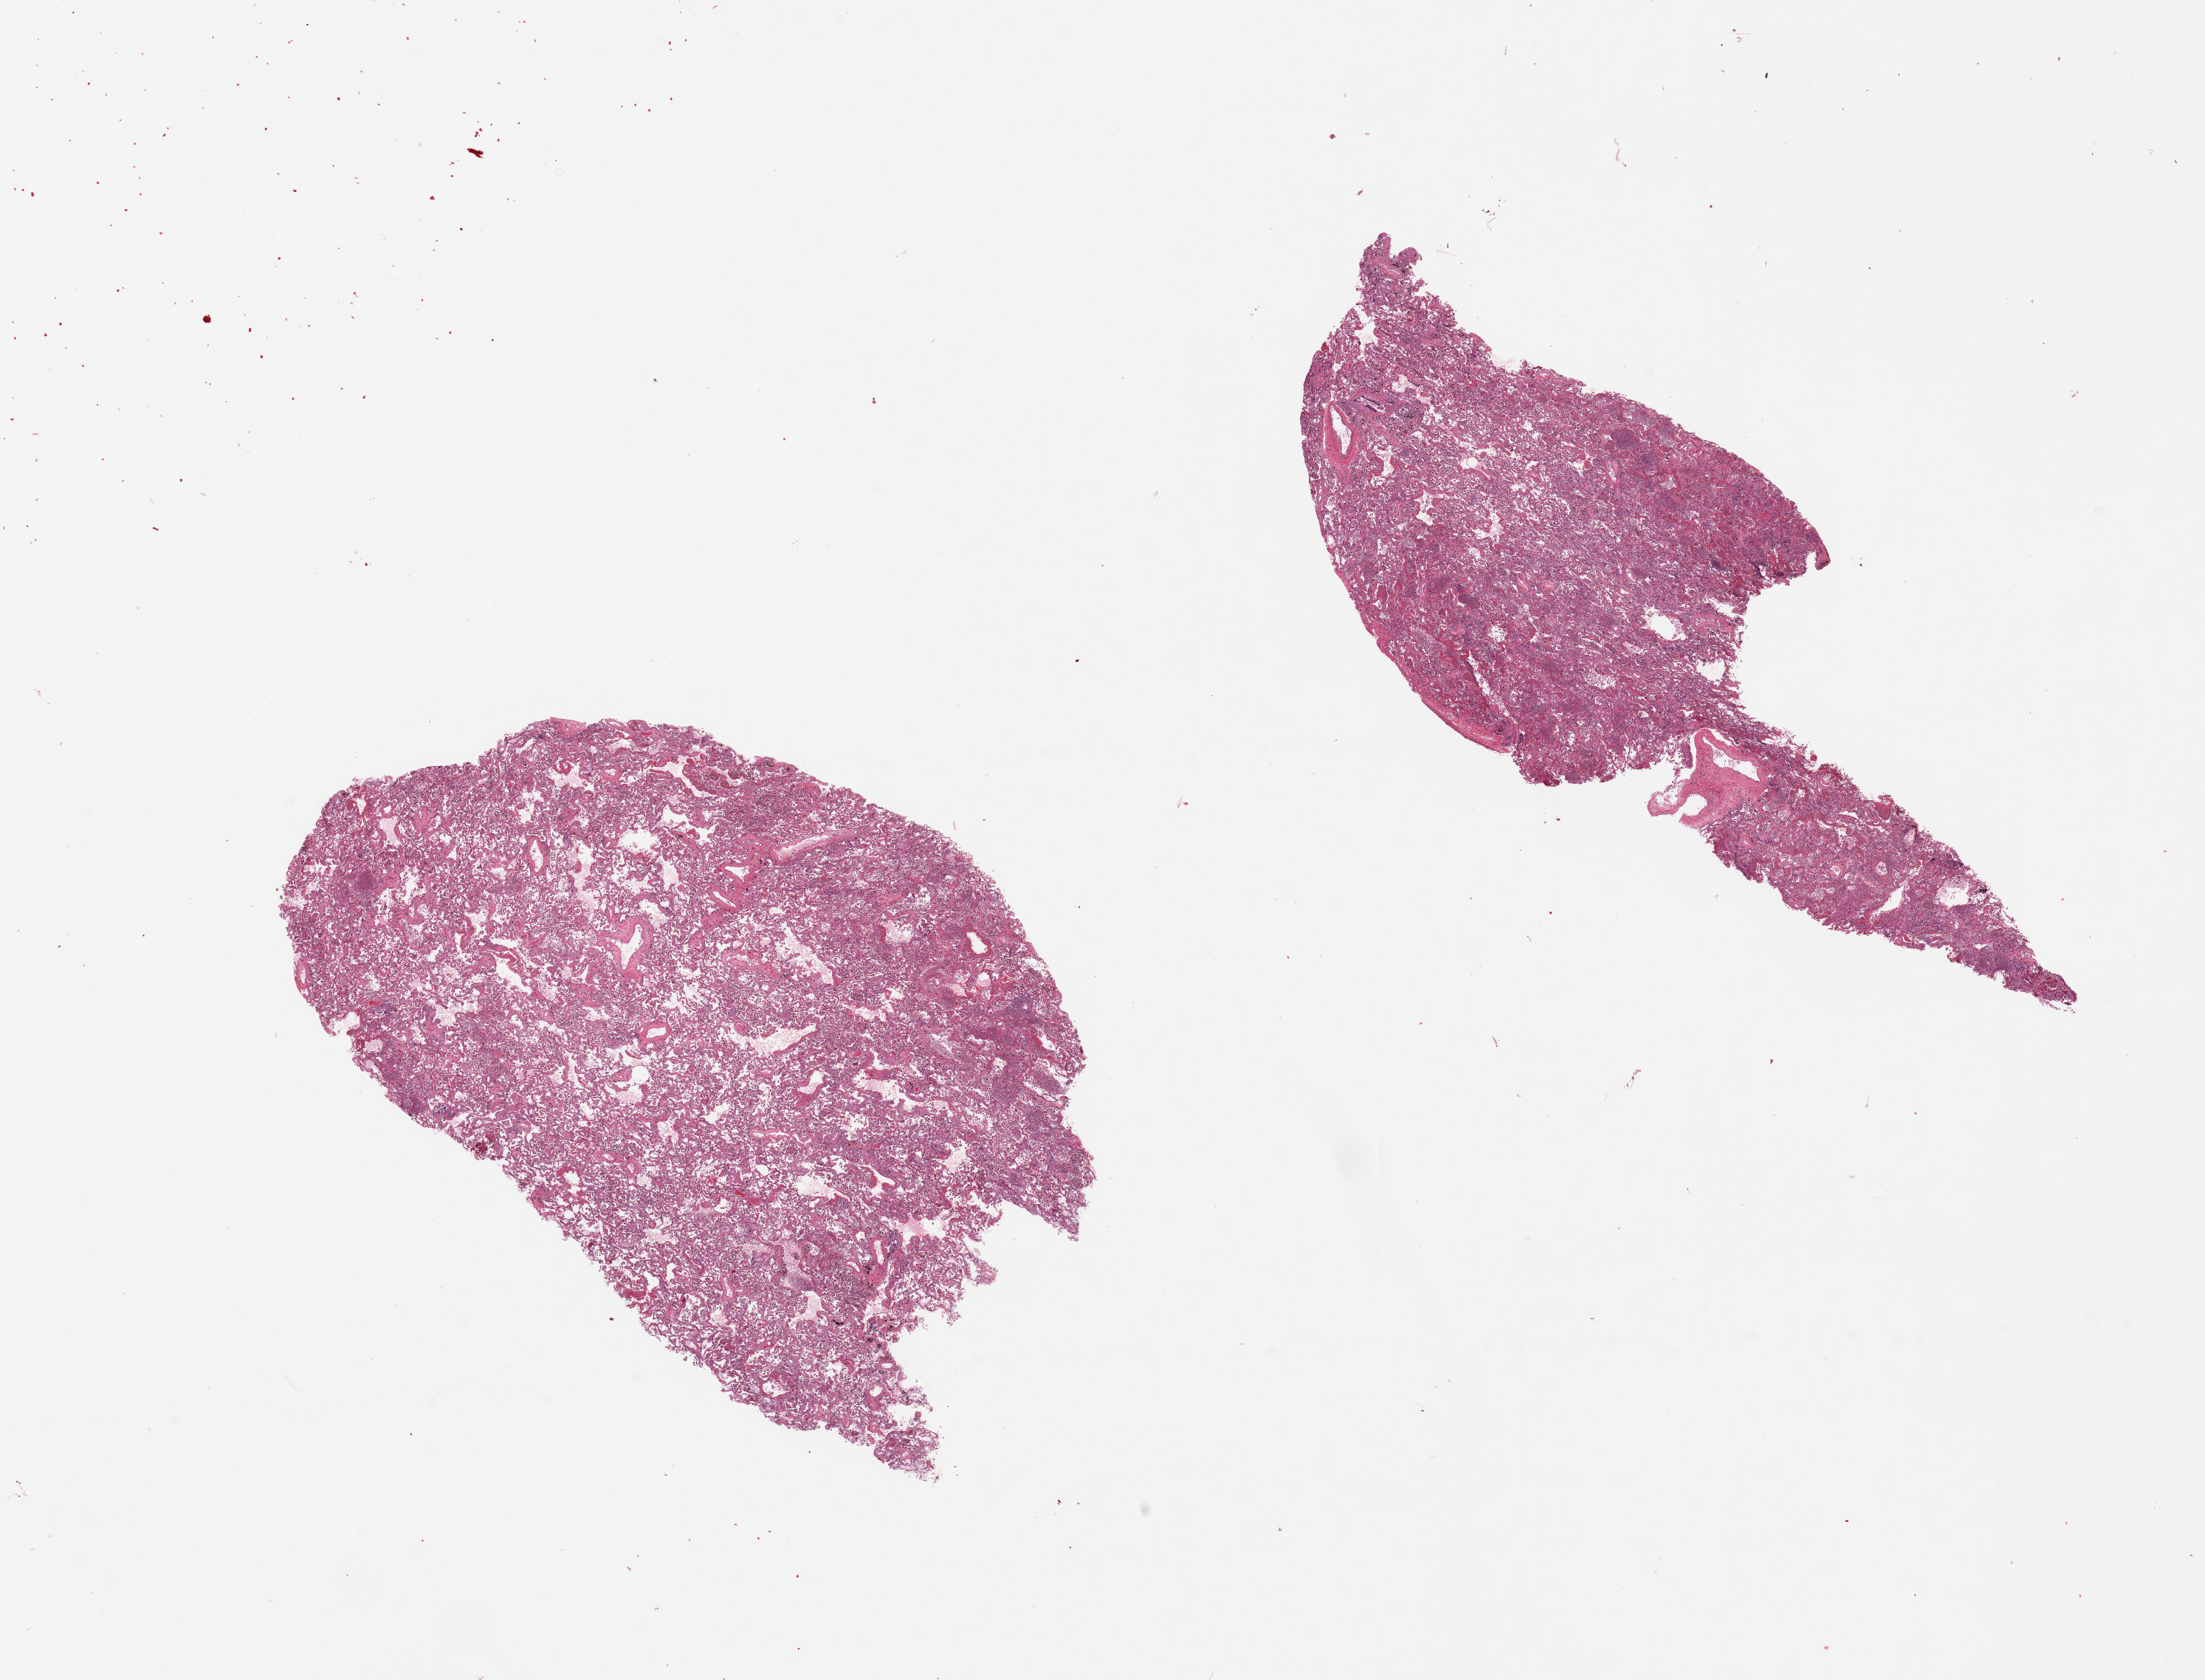
H&E whole-slide image, brightfield — whole scanned area (about 23.6 x 18.0 mm) shown as a low-resolution overview. PAXgene-fixed paraffin-embedded (PFPE) section. Sampled site (target tissue): lung. Tissue donor sample.
• pathologist's review note for this sample: 2 pieces, diffuse acute pneumonia, aggregates of polymorphonuclear leukcytes are abundant